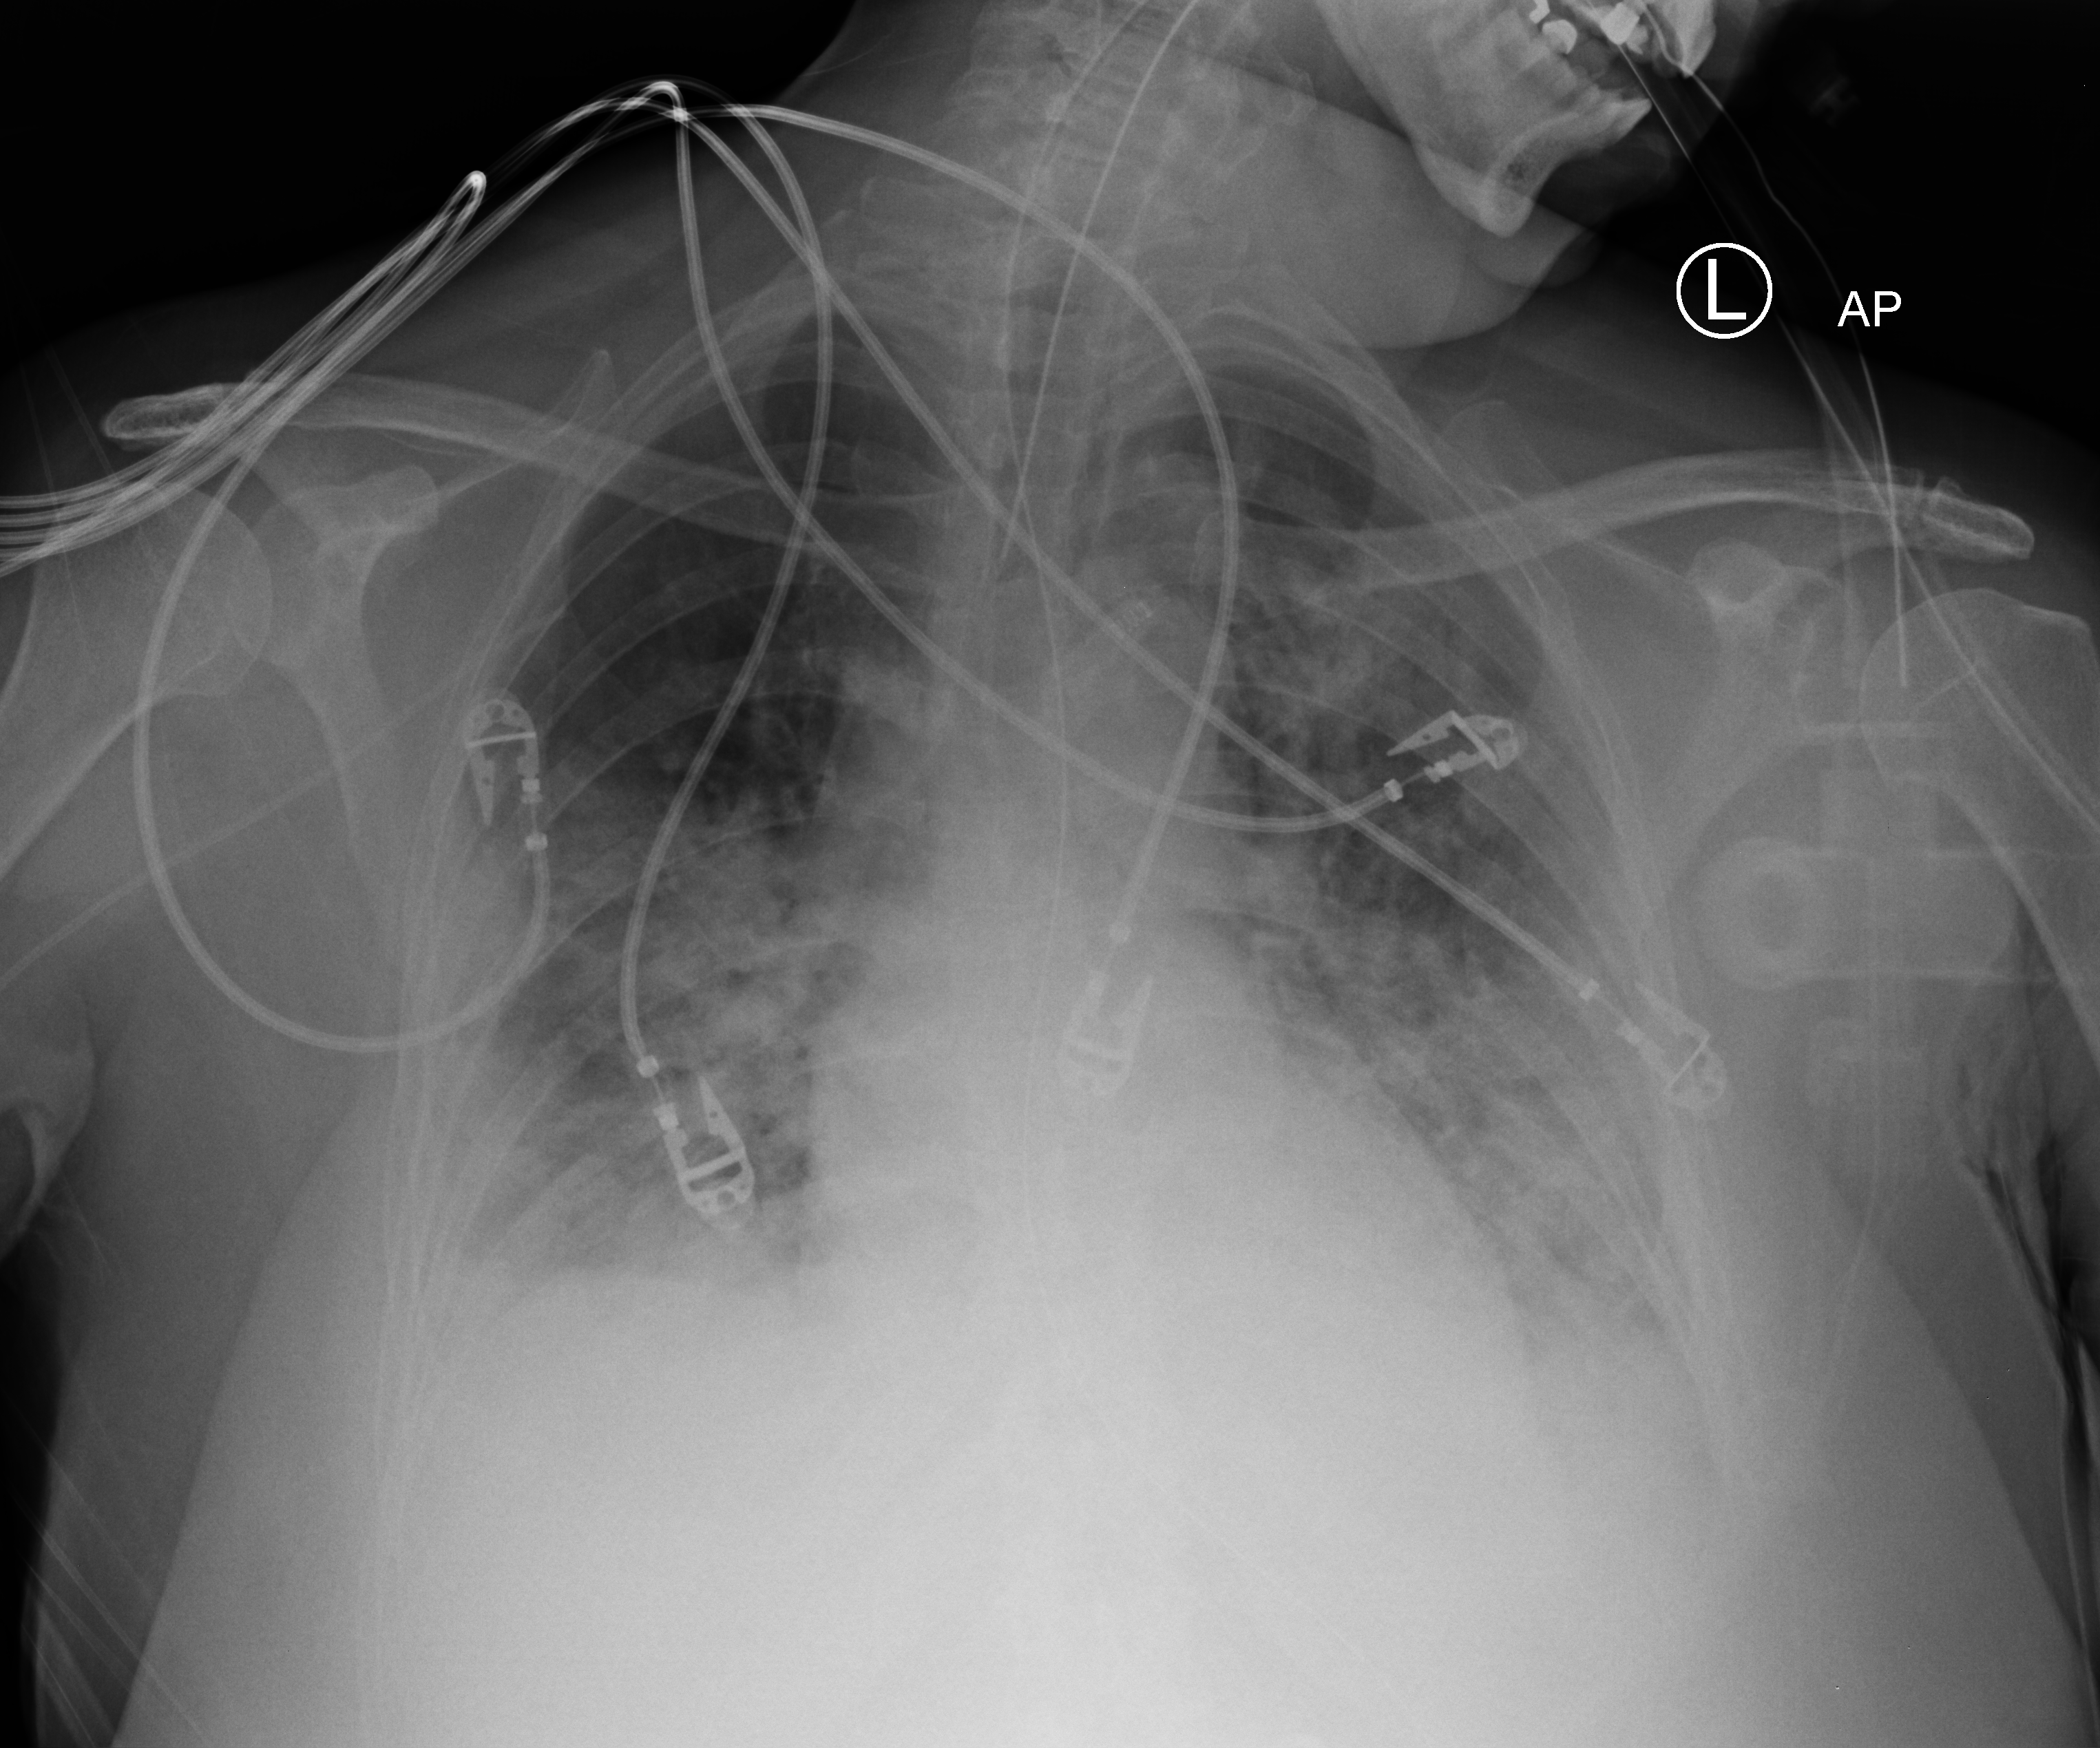
Portable chest radiograph; anteroposterior (AP) projection. Patient hospitalised with COVID-19; female, aged 18–59 years.
Admission-level facts for this patient (not findings on this image; timing relative to this image not recorded): admitted to intensive care during this hospital stay: yes; length of hospital stay: 22 days.